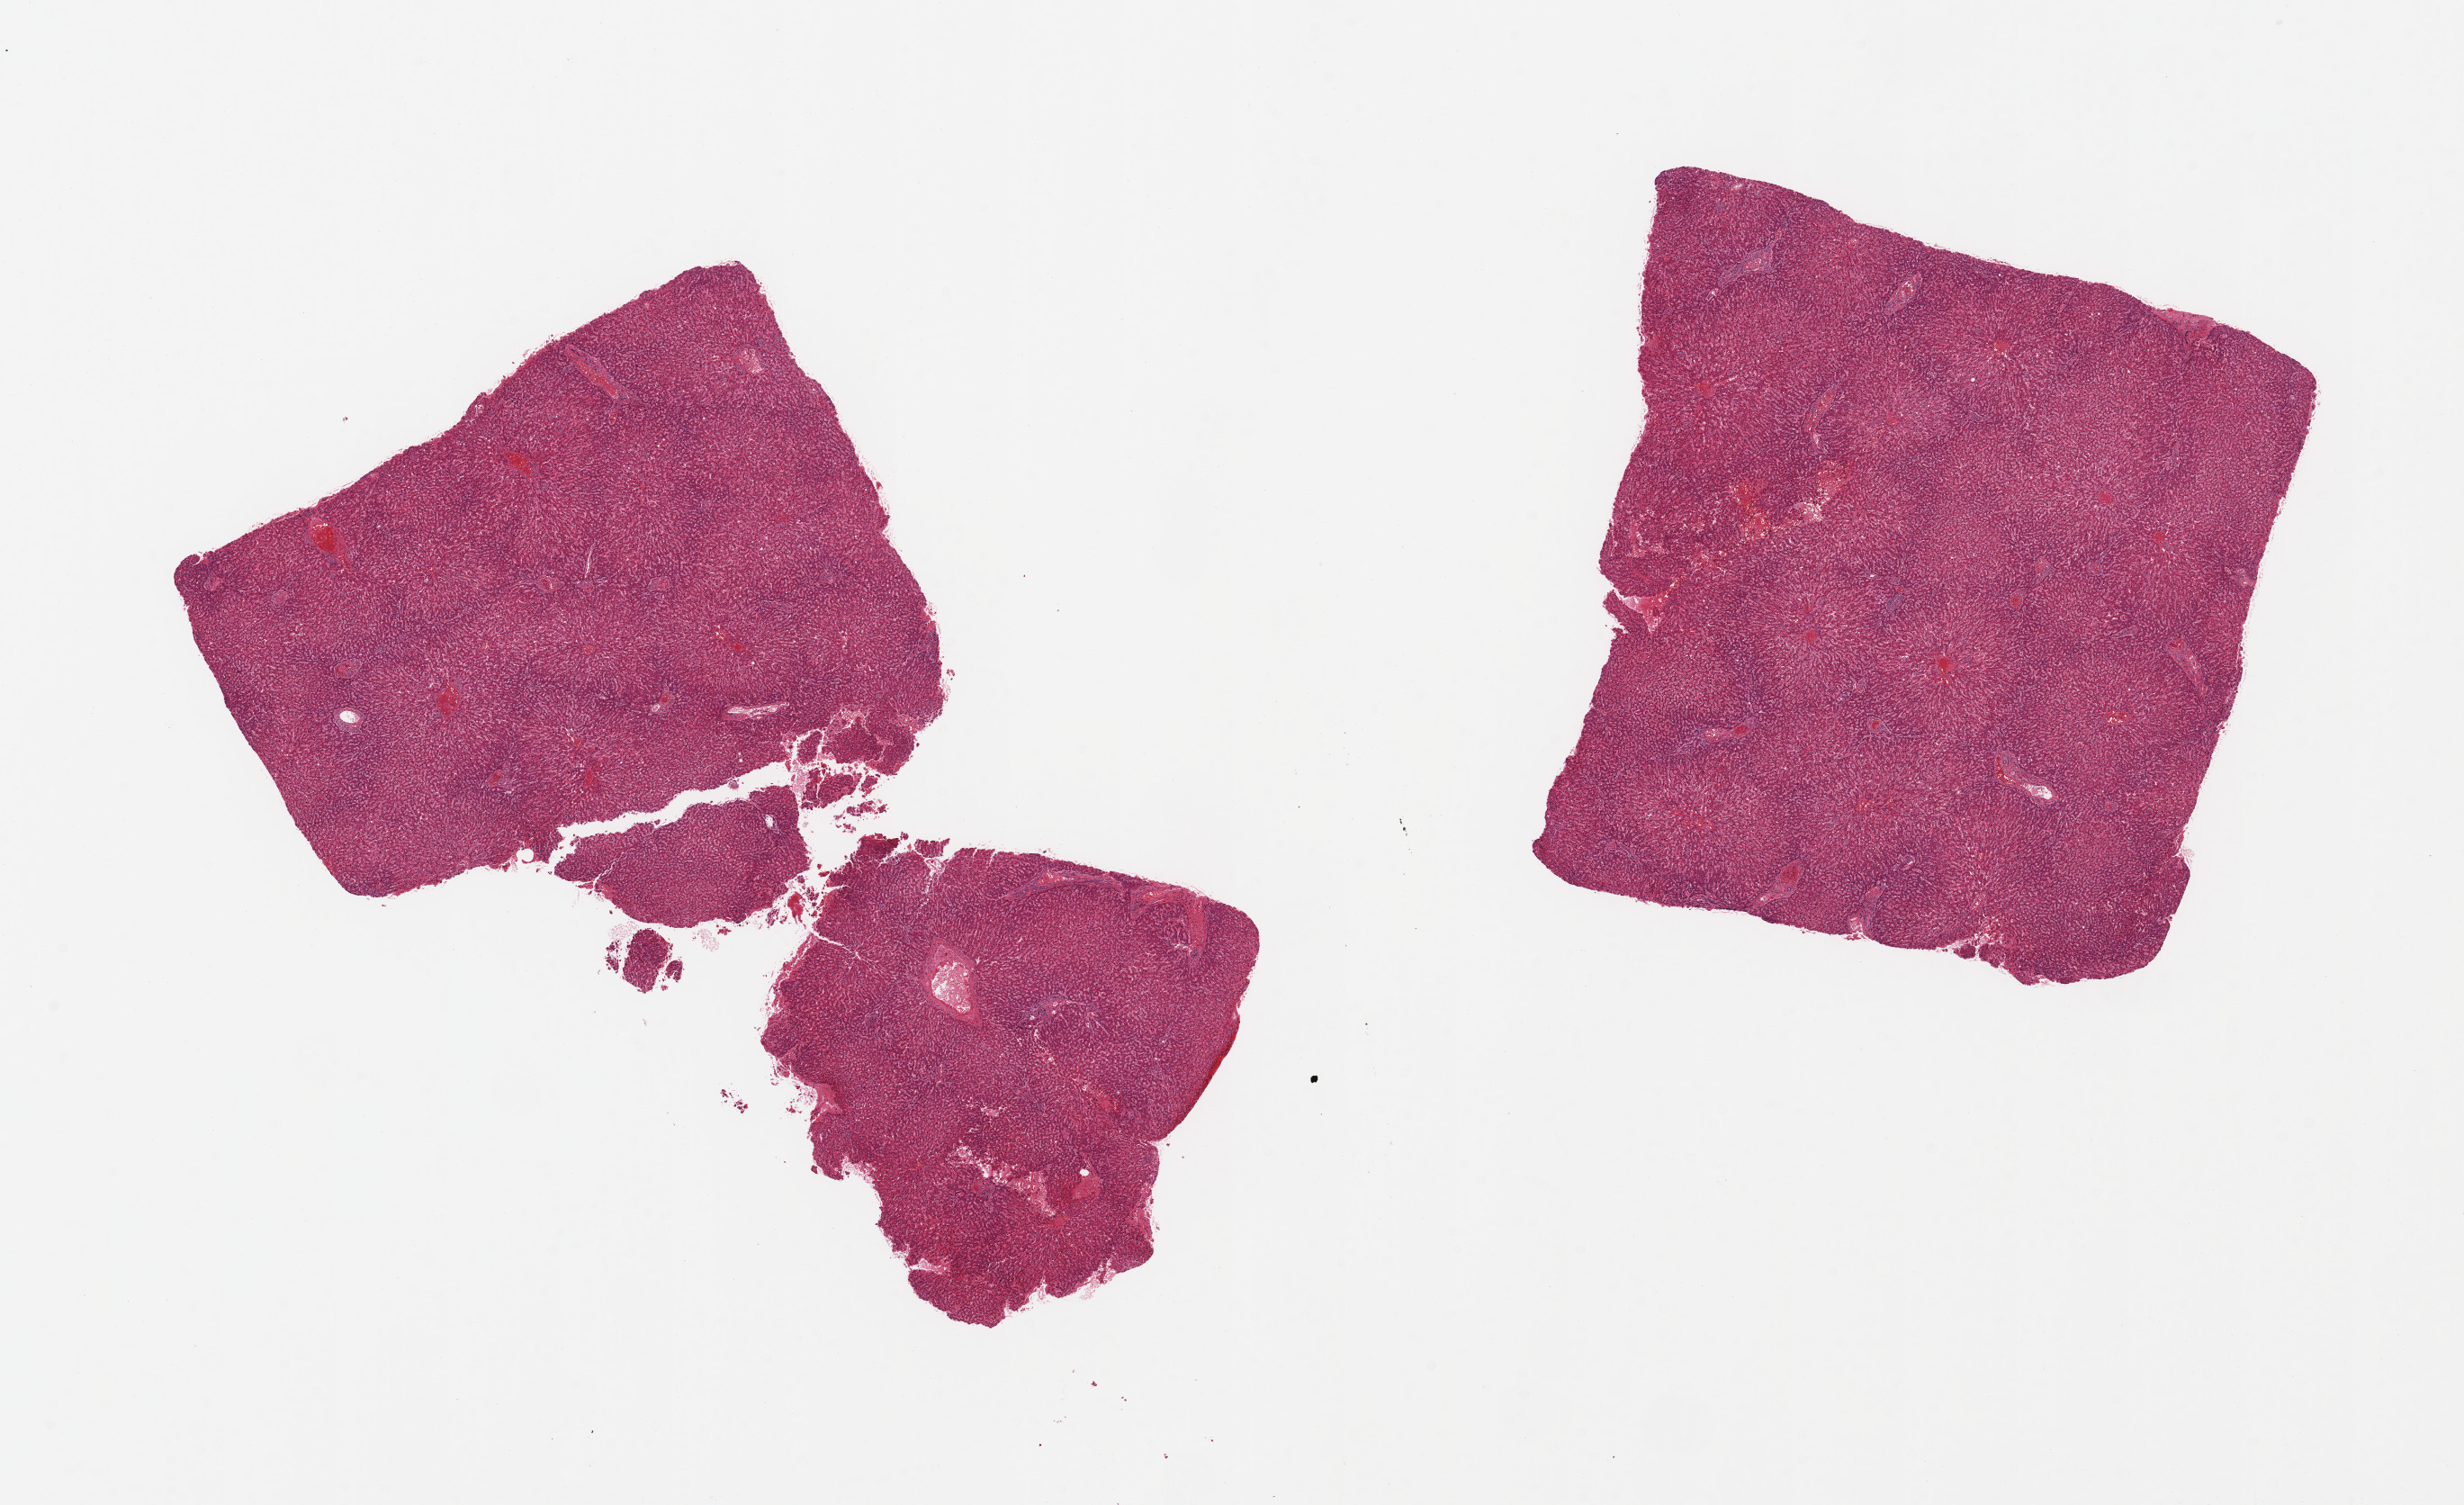
H&E whole-slide image, brightfield — whole scanned area (about 21.7 x 13.2 mm) shown as a low-resolution overview, PAXgene-fixed paraffin-embedded (PFPE) section, target tissue: liver, donor tissue sample.
Reviewer comment on this tissue sample: 2 pieces, moderate passive congestion.